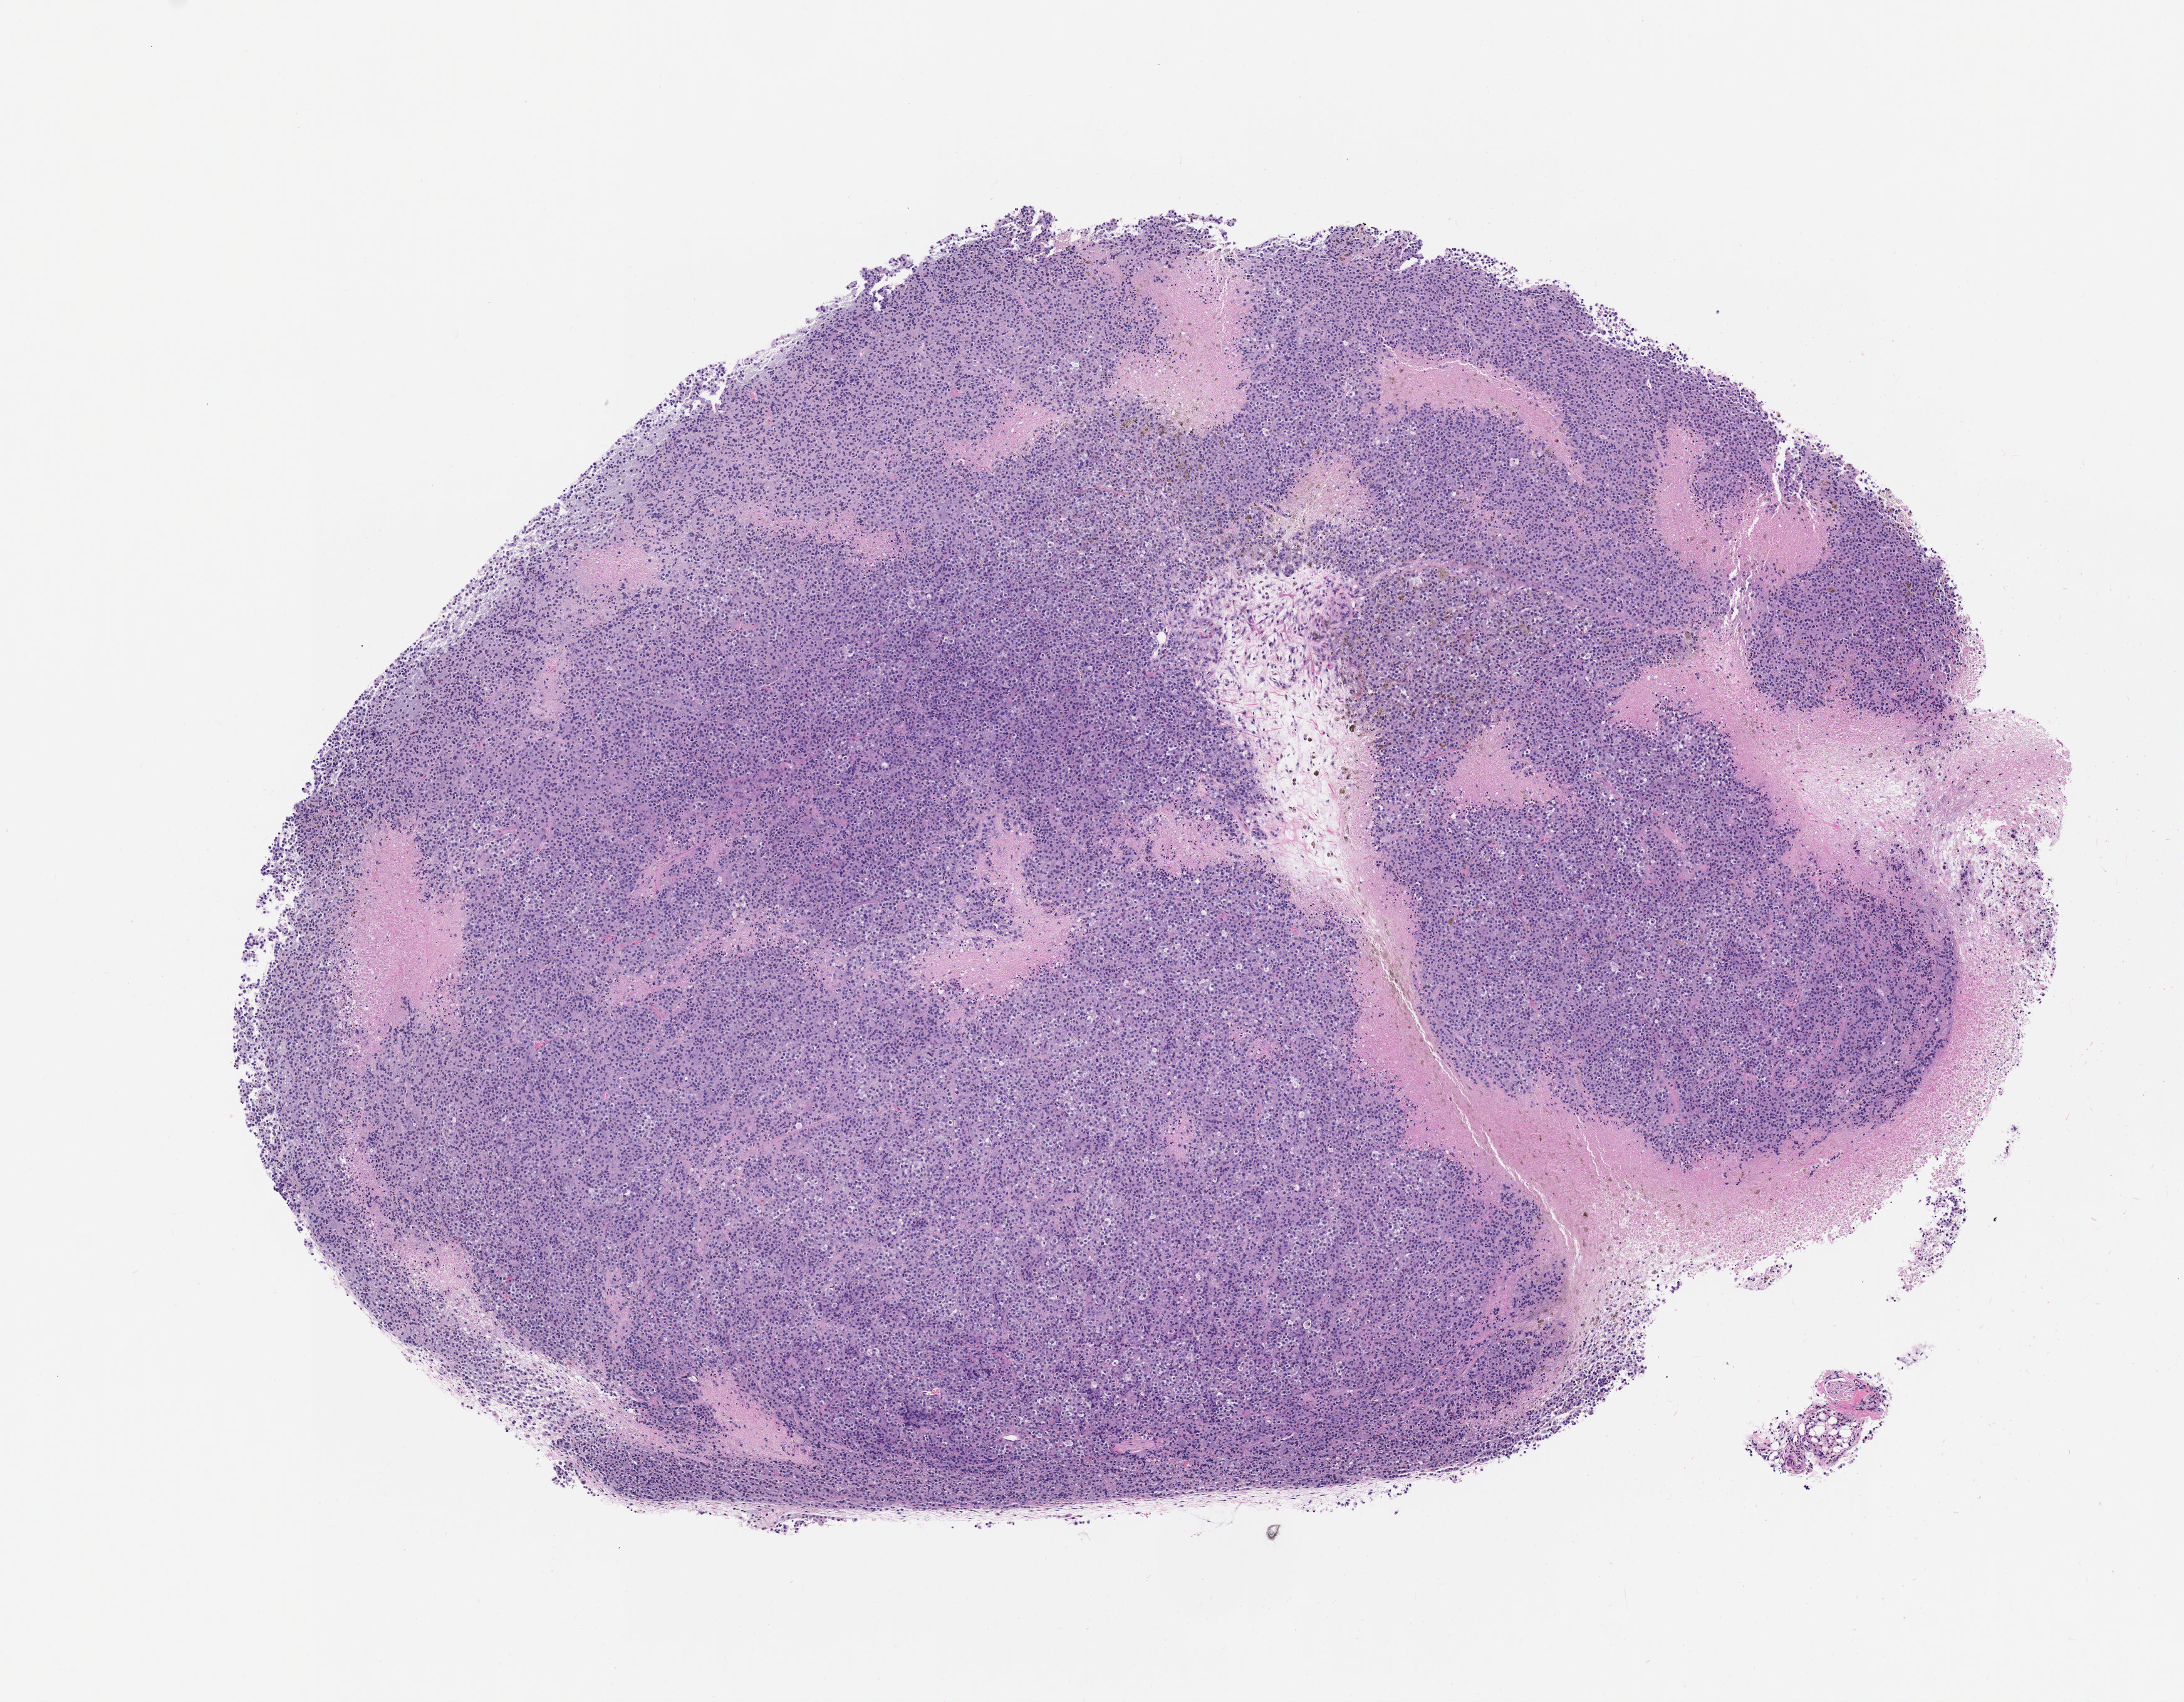
Whole-slide image, H&E: patient-derived xenograft (human tumor grown in a mouse), passage 1 — a low-resolution overview of the entire scanned area, about 7.0 x 5.5 mm. Formalin-fixed paraffin-embedded section. Originating tumor site category: skin.
Originating patient diagnosis: Melanoma.